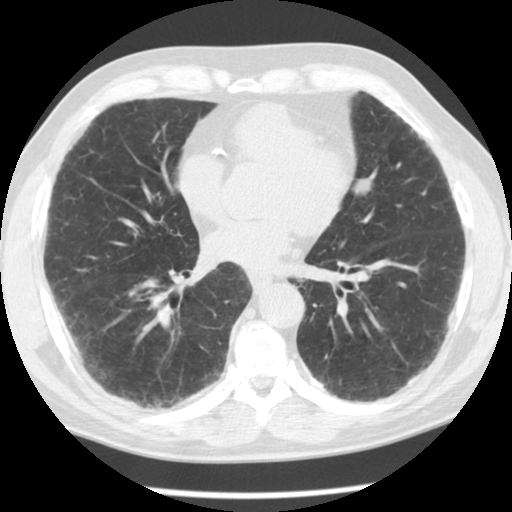
Low-dose screening chest CT, one axial slice. Position 50 of 113 along the scan axis. 120 kVp. Lung window (W 1500 / L -600 HU). 2.5 mm slice thickness. 512 × 512 image matrix, field of view 330 × 330 mm.
Structures marked on this image (outlined manually by an expert reader):
- lesion 1 (nodule, upper lobe of left lung): bounding box (x1, y1, x2, y2) in pixels: (352, 179, 372, 195)